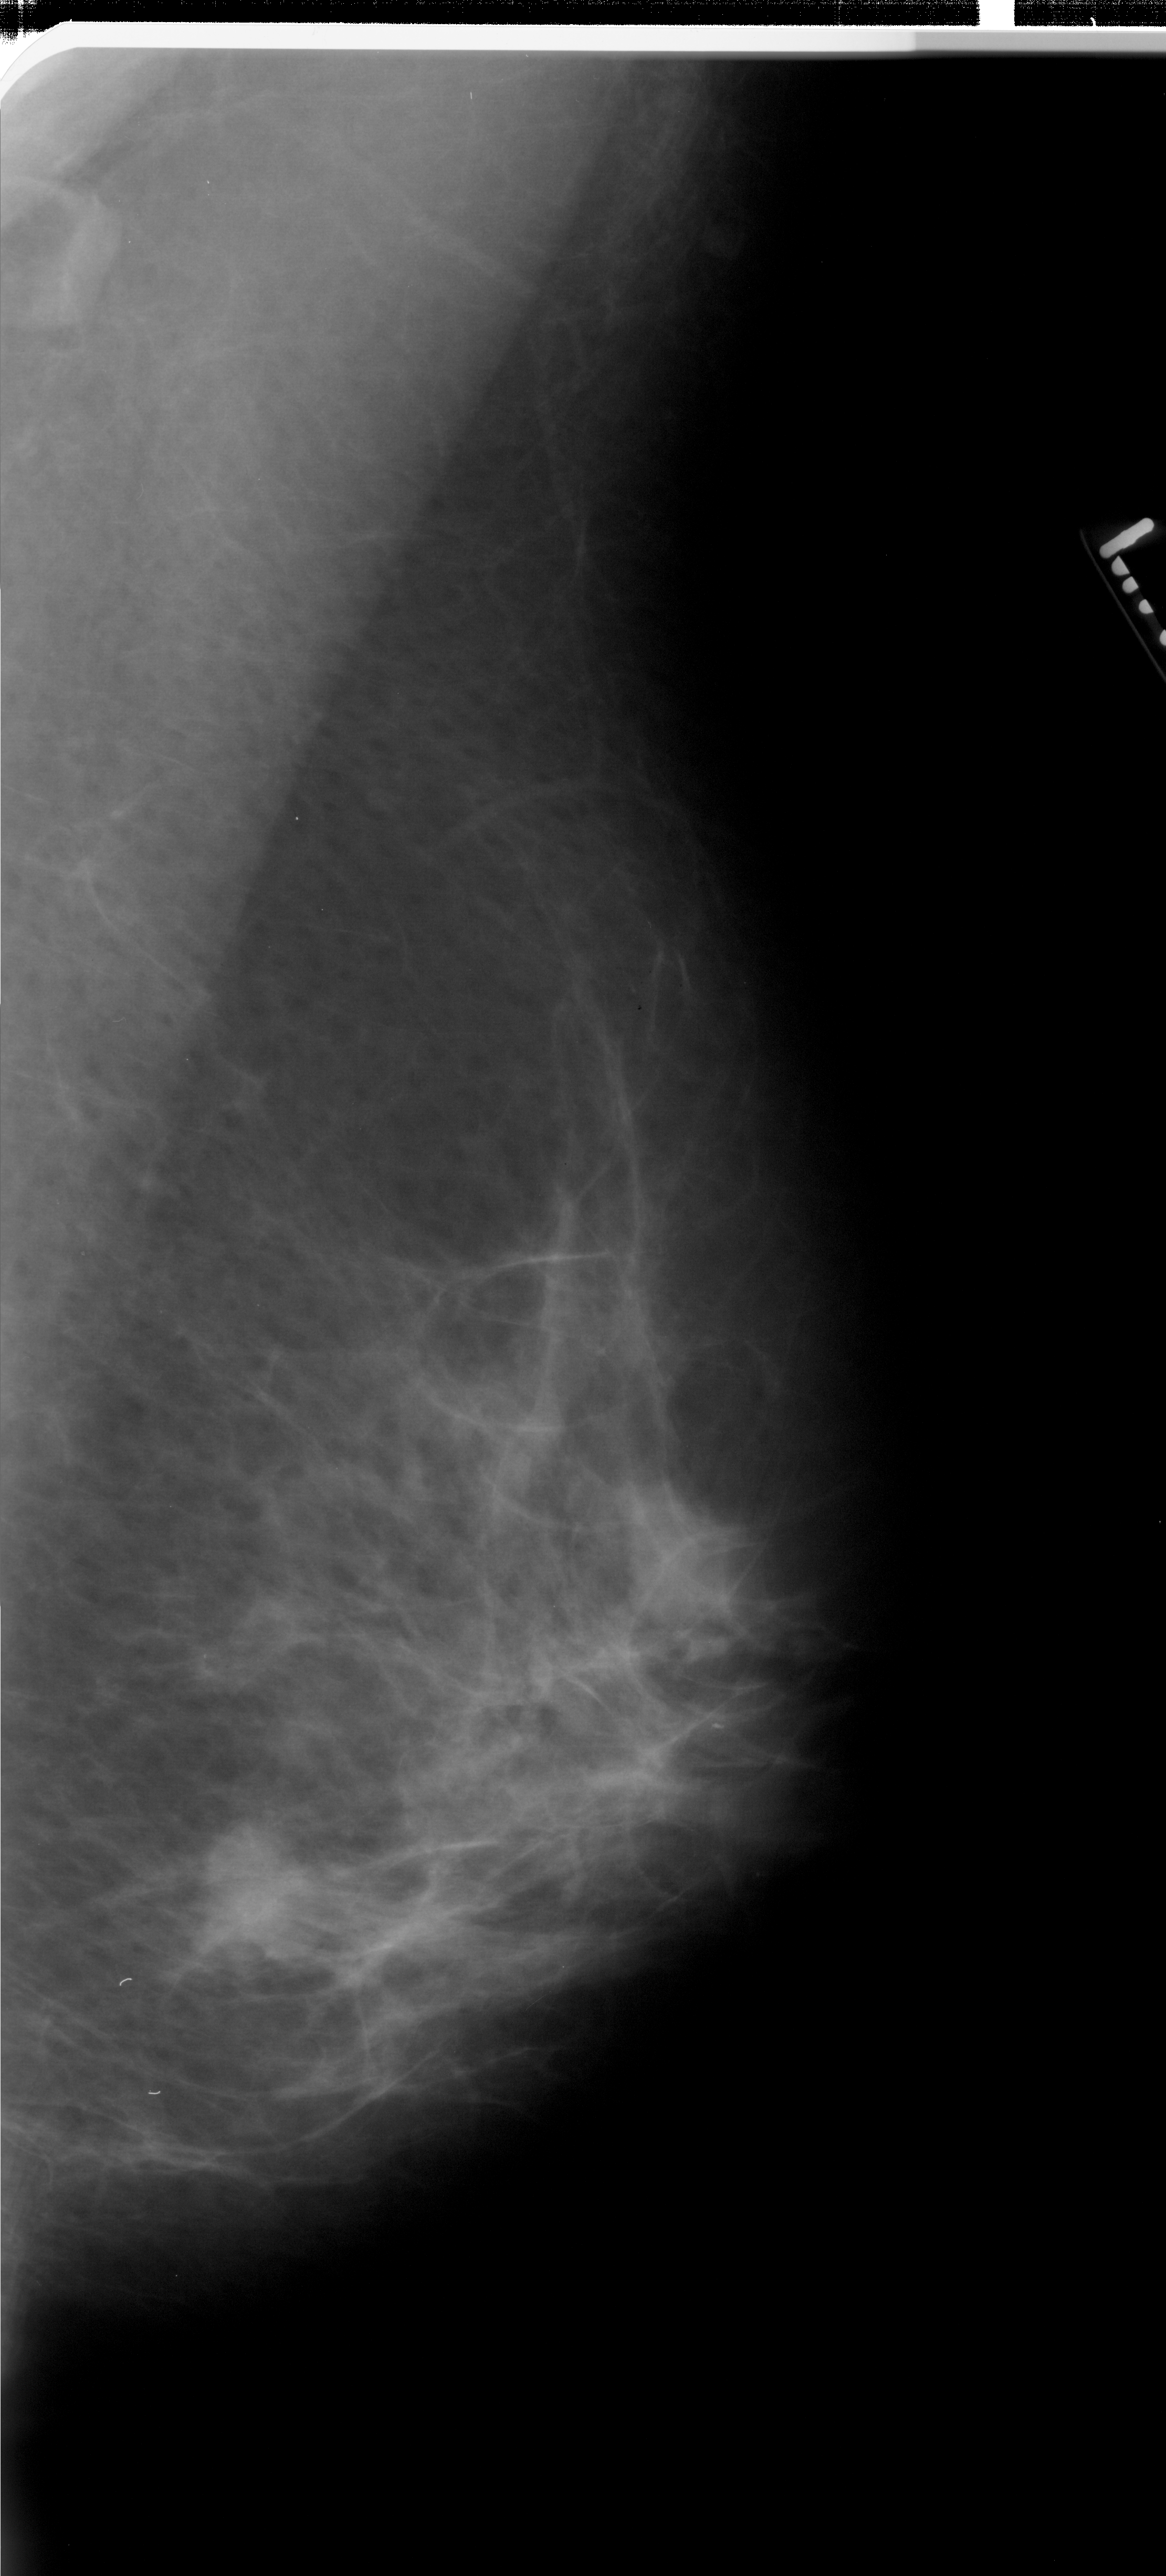
Scanned film-screen mammogram; right breast; MLO view.
- Finding: mass, shape lobulated, margins ill defined; BI-RADS assessment category 4; subtlety rating 4 on a 1 (subtle) to 5 (obvious) scale; pathology result (as recorded, not read from the image): malignant.